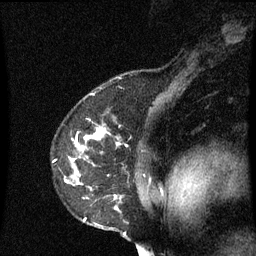
Breast MRI (dynamic contrast-enhanced), one sagittal slice; position 49 of 60 along the scan axis; dynamic contrast-enhanced series, image 2 of 3 at this slice position (ordered by acquisition); 1.5 T; TE 4.2 ms, TR 8.9 ms; 2 mm slice thickness; 256 × 256 image matrix, field of view 200 × 200 mm. Female patient, age 53 years. From the clinical record (not read from this slice): setting: breast cancer imaged before/during neoadjuvant chemotherapy; receptor status: HR-positive, HER2-negative.
Annotated regions visible in this slice (semi-automatic segmentation, software-assisted and operator-edited):
- analysis volume of interest (the breast-tissue region the enhancement analysis was run in; not a lesion): box from (x=54, y=128) to (x=157, y=231) px
- tumour enhancement mask (voxels above the 70 % enhancement threshold inside the analysis volume of interest): (x=66, y=130)–(x=105, y=219)